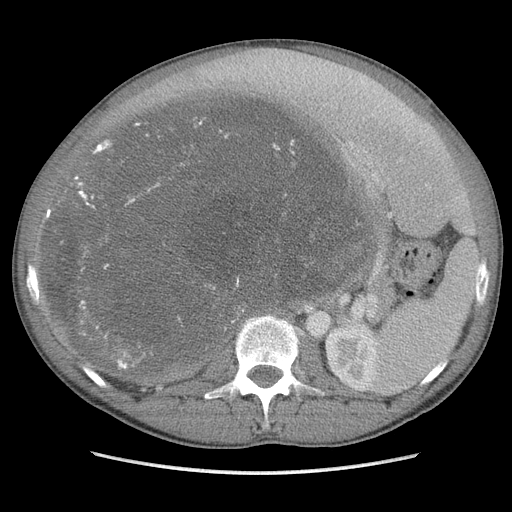
Contrast-enhanced abdominal CT, one axial slice. Slice 63 of 115 in the series (ordered by position). Soft-tissue window (W 400 / L 40 HU). 5 mm slice thickness. 512 × 512 image matrix. Male patient. Case-level facts recorded for this patient, not image findings: diagnosis: adrenocortical carcinoma; tumour side: right adrenal; Ki-67 index: 13 %; stage (as recorded): 3.
Annotated regions visible in this slice (semi-automatically segmented with operator editing):
- mass: box from (x=43, y=96) to (x=368, y=374) px